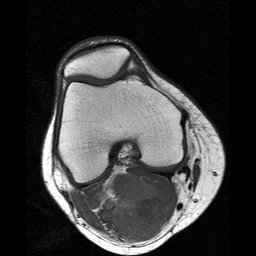
MRI of an extremity soft-tissue mass, one axial slice. Position 9 of 25 along the scan axis. 256 × 256 image matrix, field of view 160 × 160 mm. Female patient. Case-level facts recorded for this patient, not image findings: histological type: liposarcoma; site of the primary tumour: right thigh.
Structures marked on this image (outlined manually by an expert reader):
- gross tumour volume (mass): bounding box [x1, y1, x2, y2] px = [95, 173, 168, 239]